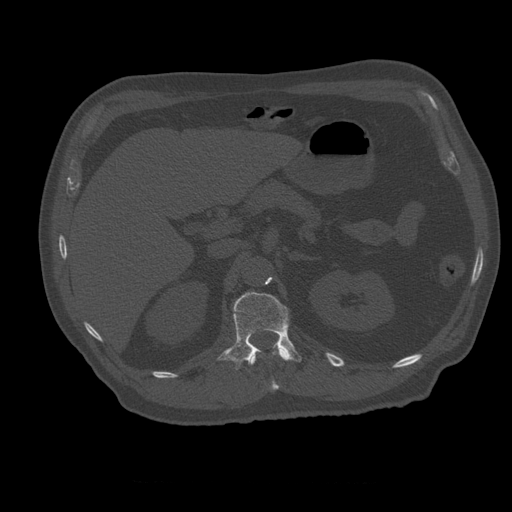
CT including the spine, one axial slice; position 243 of 399 along the scan axis; bone window (W 1800 / L 400 HU); 512 × 512 image matrix. Patient age 73 years. Case-level facts recorded for this patient, not image findings: primary cancer: prostate; vertebrae with lytic lesions (as recorded): L2.
Outlined on this slice (semi-automatically segmented with operator editing):
- L1 vertebra: bounding box (x1, y1, x2, y2) in pixels: (217, 292, 302, 370)
- T12 vertebra: (248, 343, 292, 391)